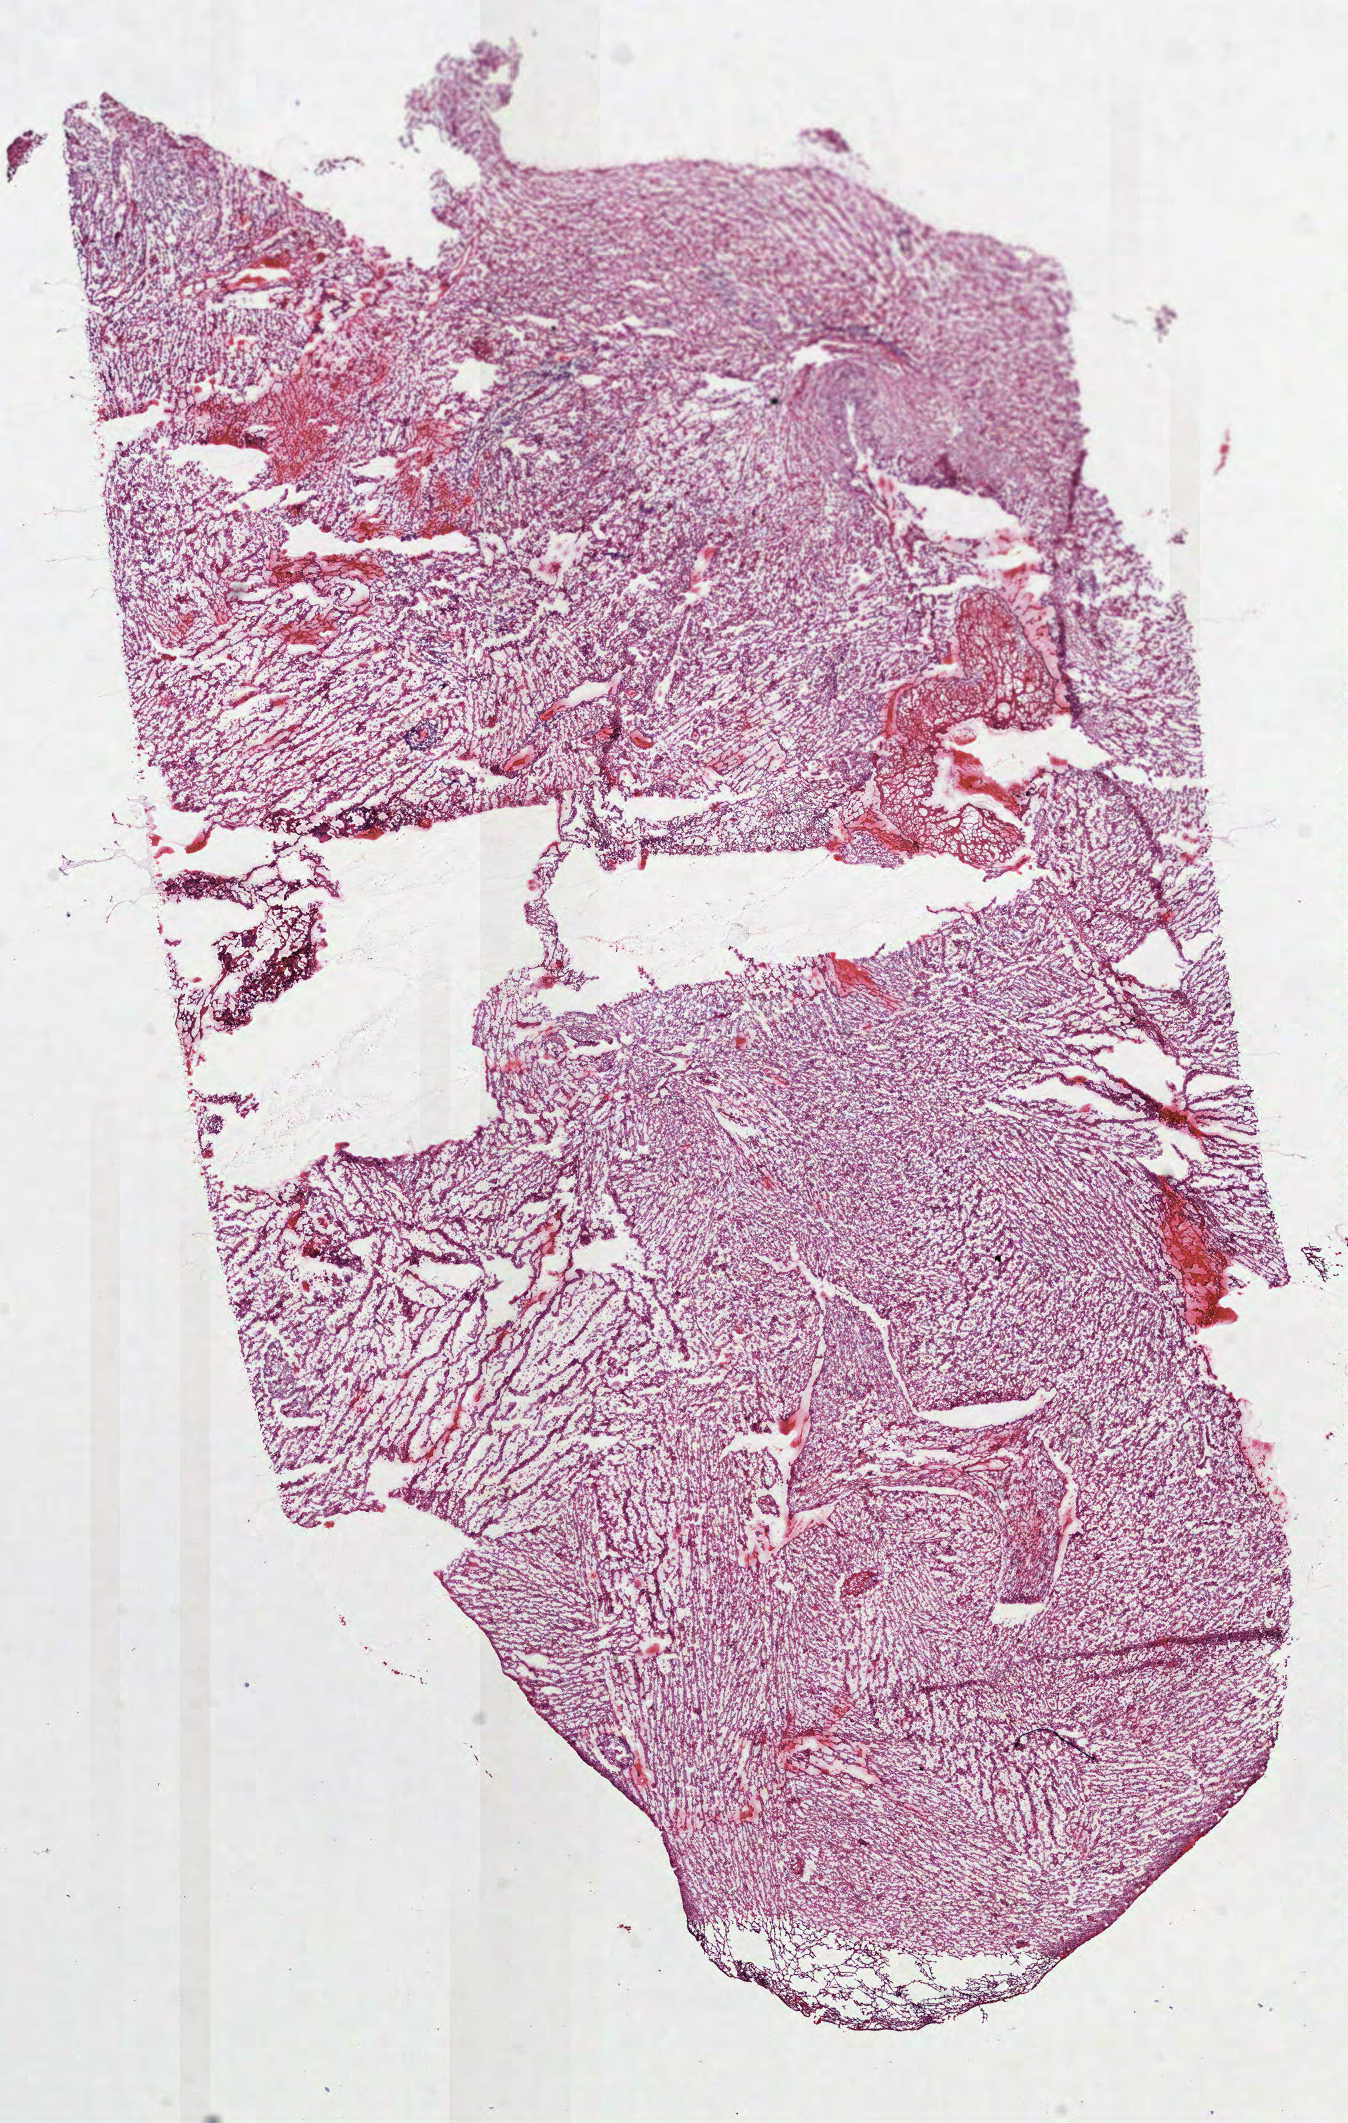
H&E-stained whole-slide image — shown as a low-resolution overview of the whole scanned area (about 10.9 x 17.1 mm, acquisition: 40x scan), frozen section from the top of the tissue portion, primary tumour sample from the brain. Patient: male, age at initial diagnosis 63 years. Composition of this section per pathologist review: tumour cells 100%, tumour nuclei 75%, normal cells 0%, stromal cells 0%, necrosis 0%.
Pathologic diagnosis: Glioblastoma.